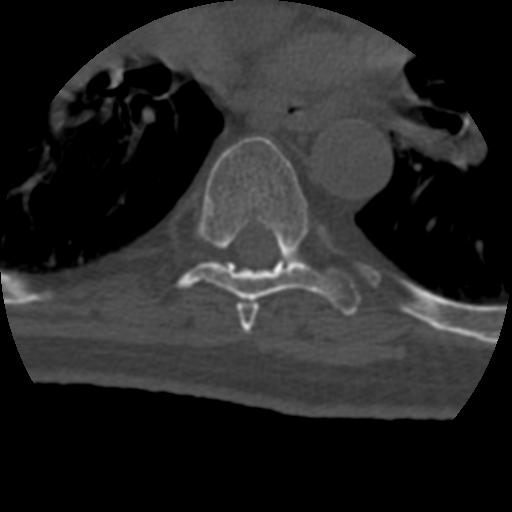
CT including the spine, one axial slice; slice 282 of 399 in the series (ordered by position); bone window (W 1800 / L 400 HU); 1.25 mm slice thickness; 512 × 512 image matrix, field of view 160 × 160 mm. Patient age 69 years. From the clinical record (not read from this slice): primary cancer: prostate.
Annotated regions visible in this slice (semi-automatic segmentation, software-assisted and operator-edited):
- T6 vertebra: bounding box <236,302,258,334> (left, top, right, bottom; pixels)
- T7 vertebra: <178,136,360,315>